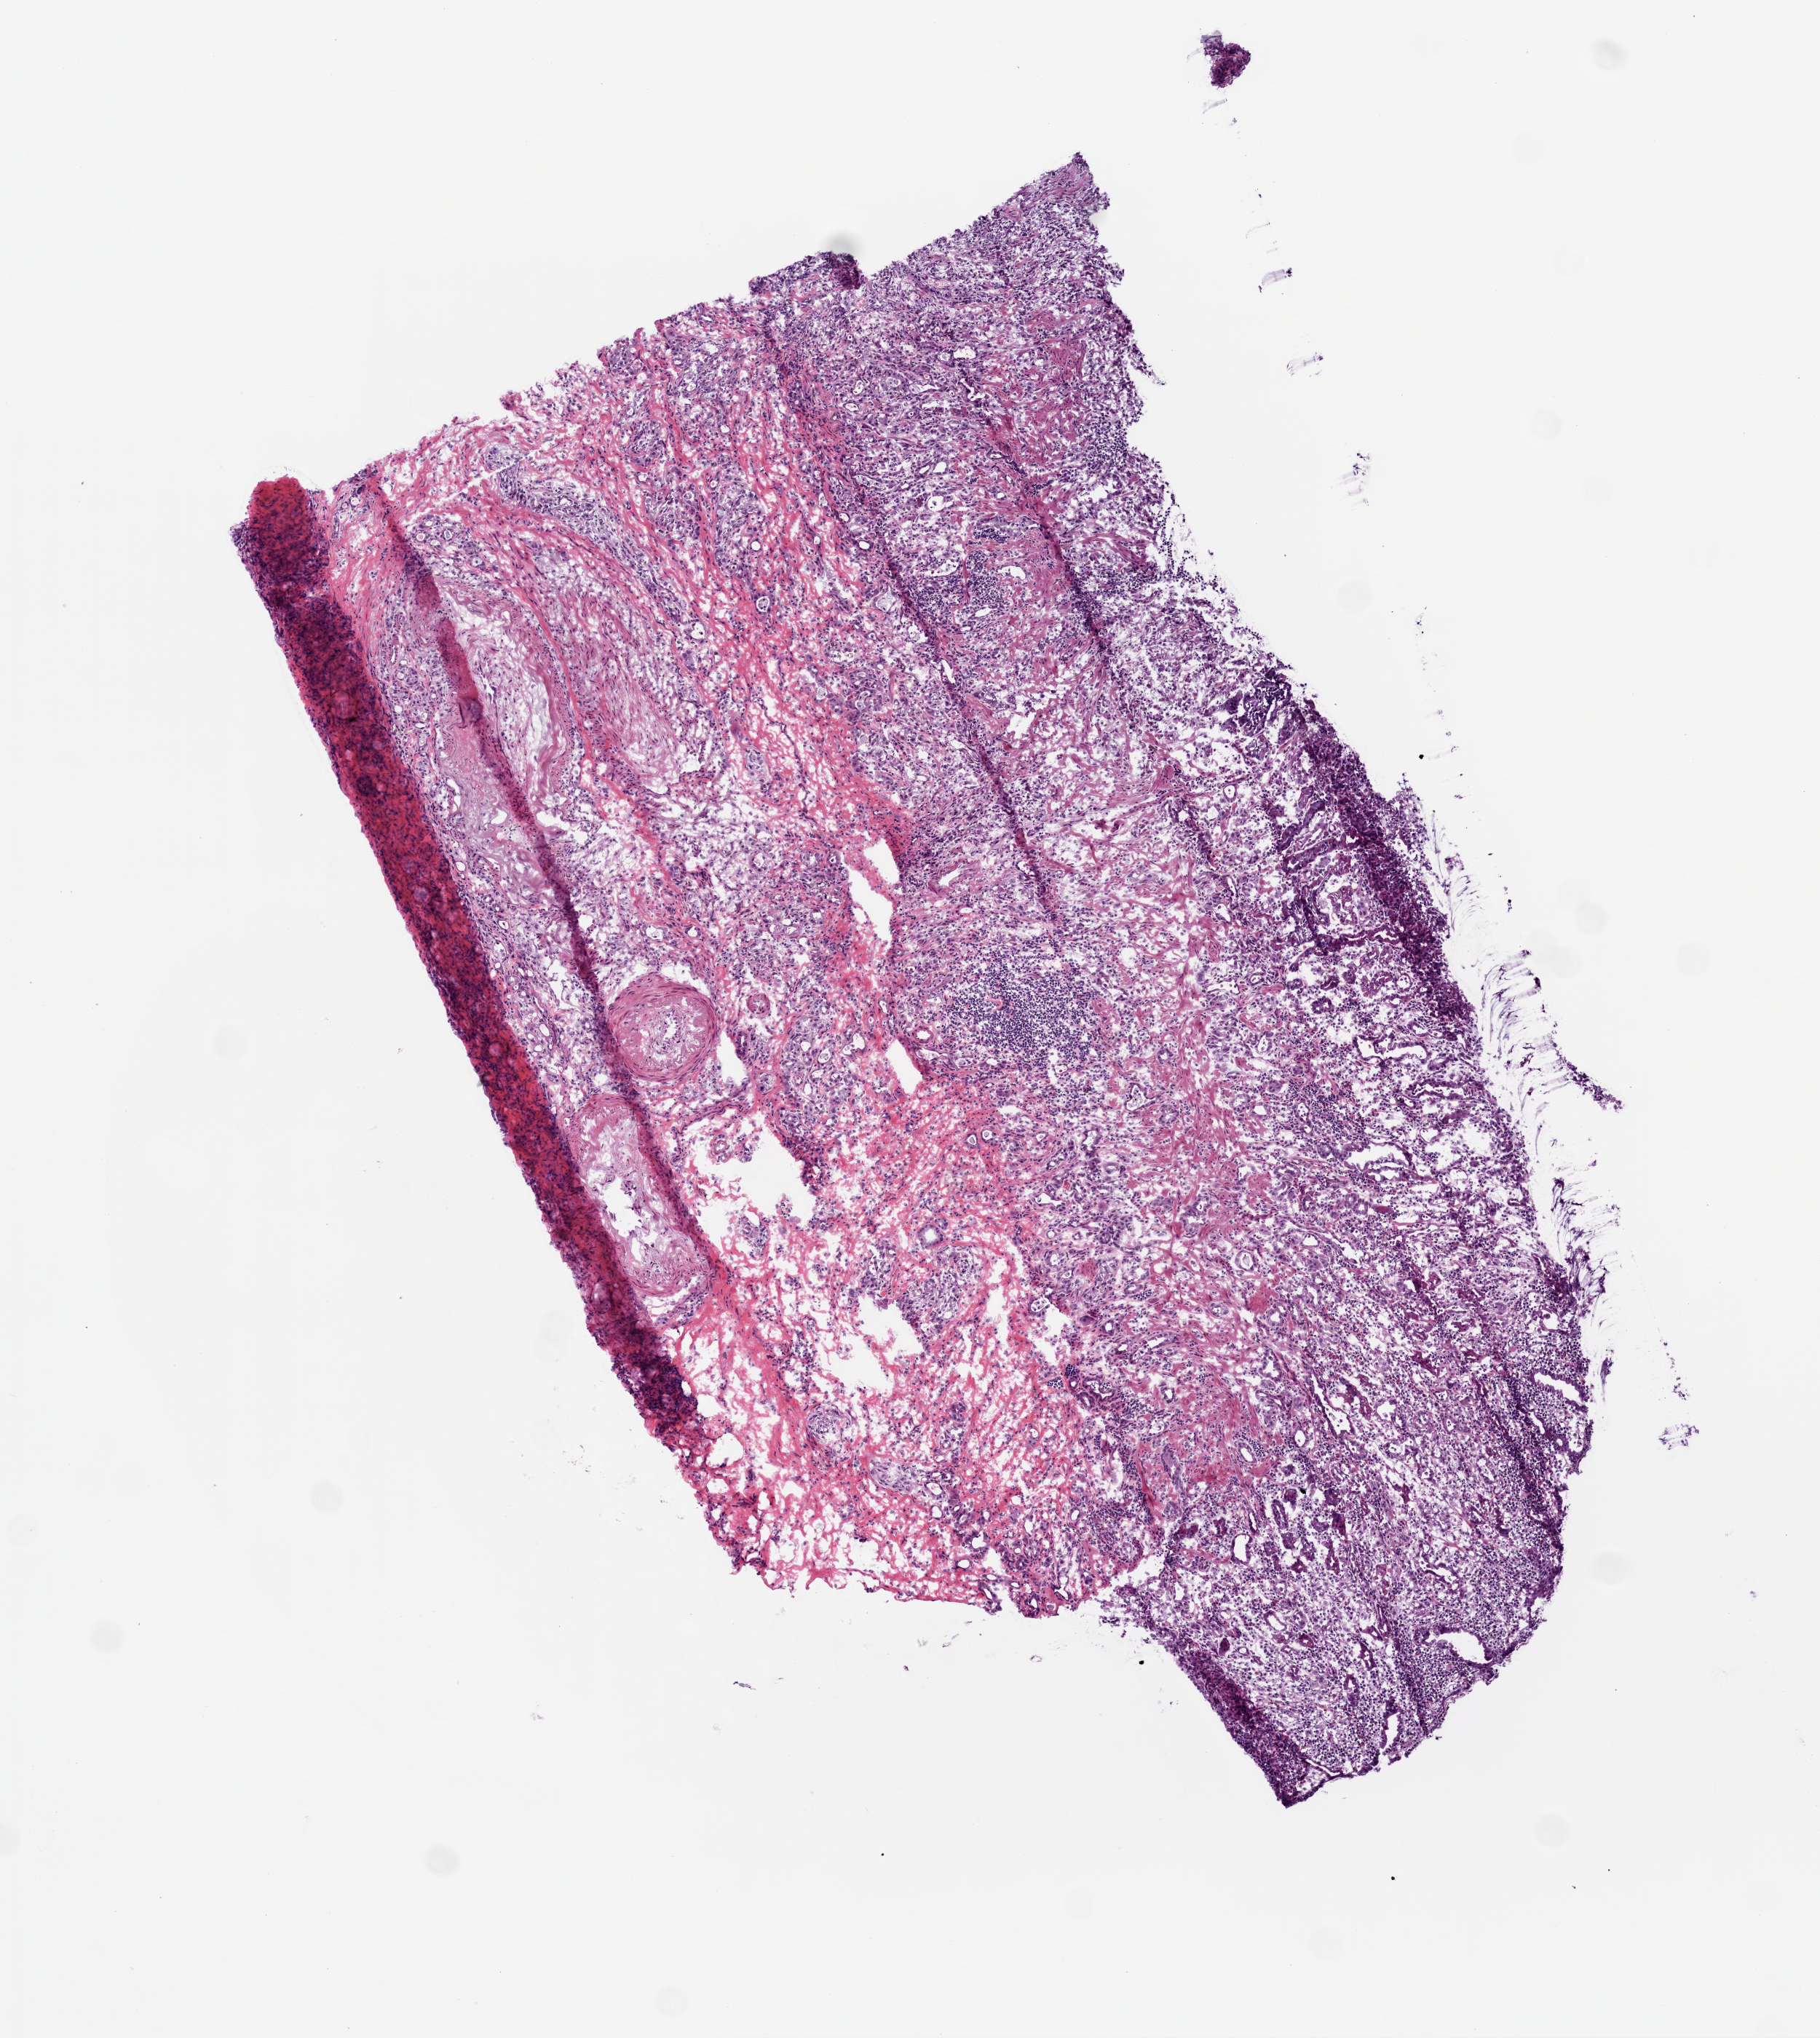
H&E whole-slide image, a low-resolution overview of the entire scanned area, about 5.0 x 5.6 mm (acquisition: 20x scan), frozen section, primary tumour sample from the stomach. Male, age 85 years at initial diagnosis. Histologic grade: G2 (moderately differentiated). Slide review estimates, as recorded: tumour cells 85%, tumour nuclei 70%, normal cells 0%, stromal cells 15%, necrosis 0%.
* diagnosis: Adenocarcinoma, NOS (gastric antrum)
* AJCC pathologic stage: IV (7th edition)